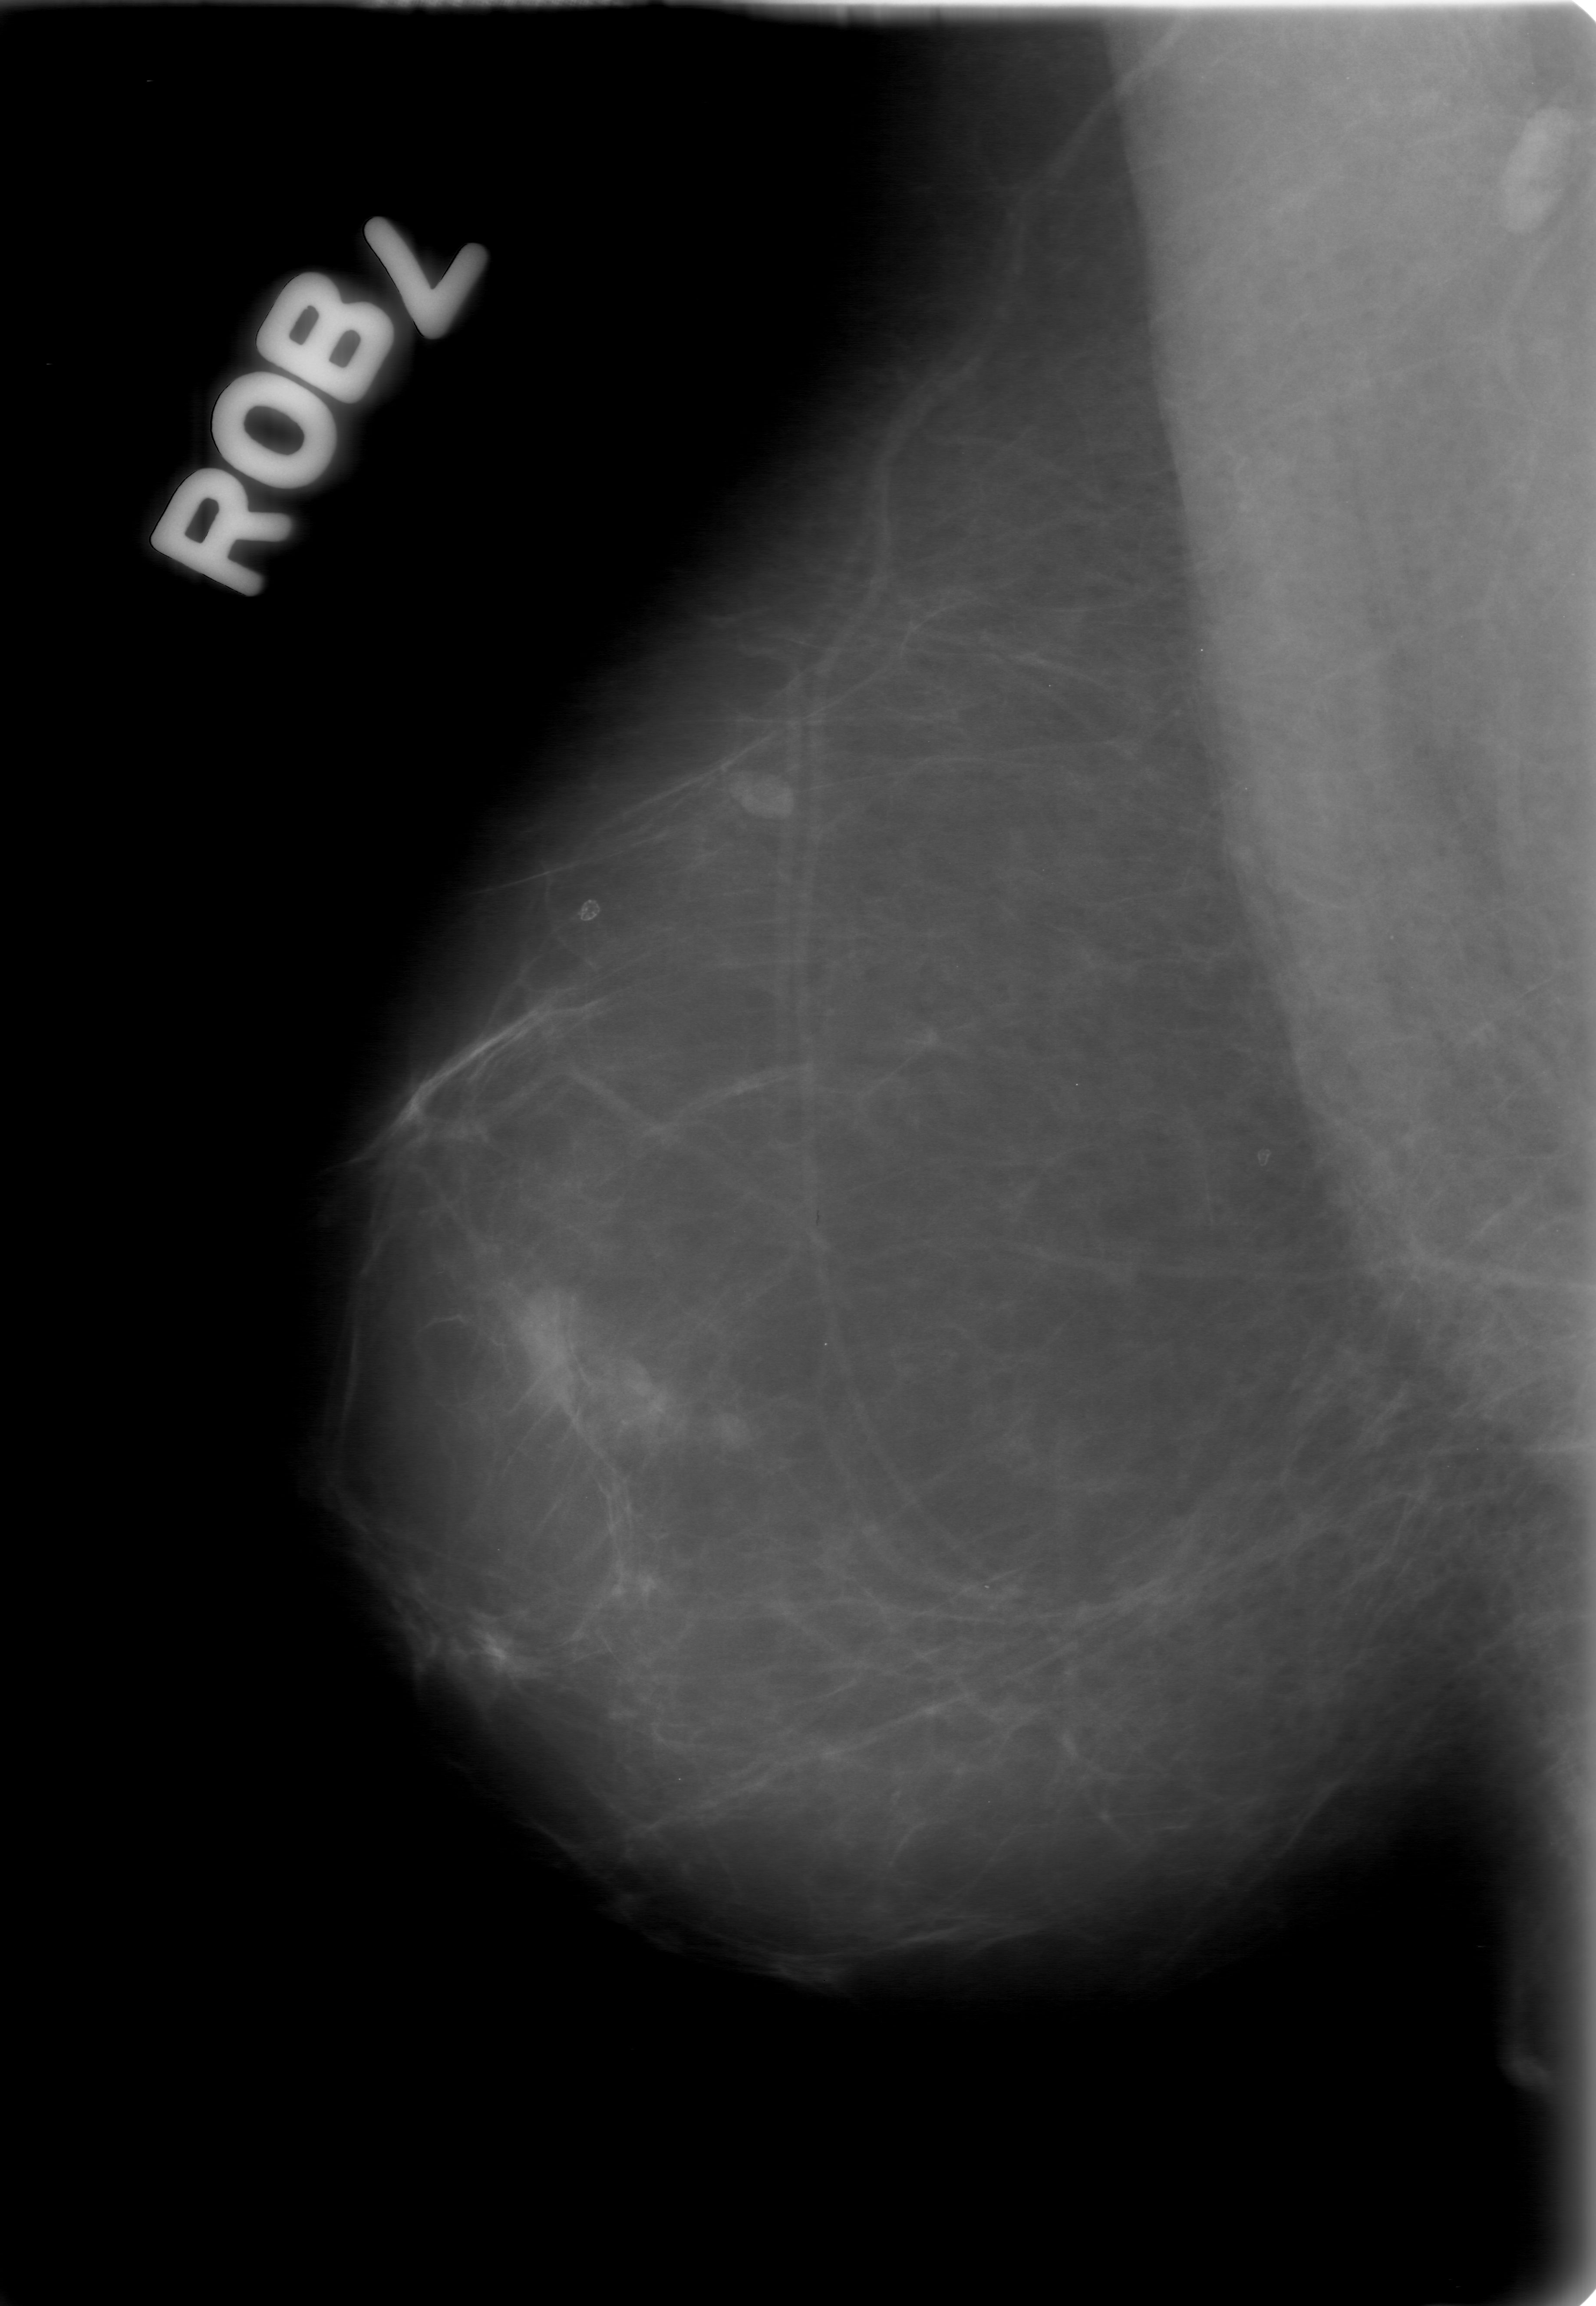
Scanned film-screen mammogram; right breast; MLO view; 1596 × 2306 image matrix.
Marked abnormalities (boxes around the expert regions of interest):
- mass, shape lobulated, margins obscured; BI-RADS assessment category 0 (incomplete: needs additional imaging); subtlety rating 2 on a 1 (subtle) to 5 (obvious) scale; pathology result (as recorded, not read from the image): benign: bounding box (x1, y1, x2, y2) in pixels: (501, 1285, 640, 1445)